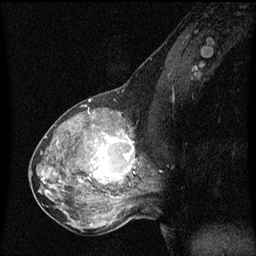
Breast MRI (dynamic contrast-enhanced), one sagittal slice; slice 31 of 60 in the series (ordered by position); dynamic contrast-enhanced series, image 2 of 3 at this slice position (ordered by acquisition); 1.5 T; TE 4.2 ms, TR 8 ms; 256 × 256 image matrix, field of view 200 × 200 mm. Female patient, age 50 years.
Outlined on this slice (semi-automatic segmentation, software-assisted and operator-edited):
- analysis volume of interest (the breast-tissue region the enhancement analysis was run in; not a lesion): box from (x=91, y=126) to (x=140, y=189) px
- tumour enhancement mask (voxels above the 70 % enhancement threshold inside the analysis volume of interest): (x=91, y=134)–(x=135, y=181)